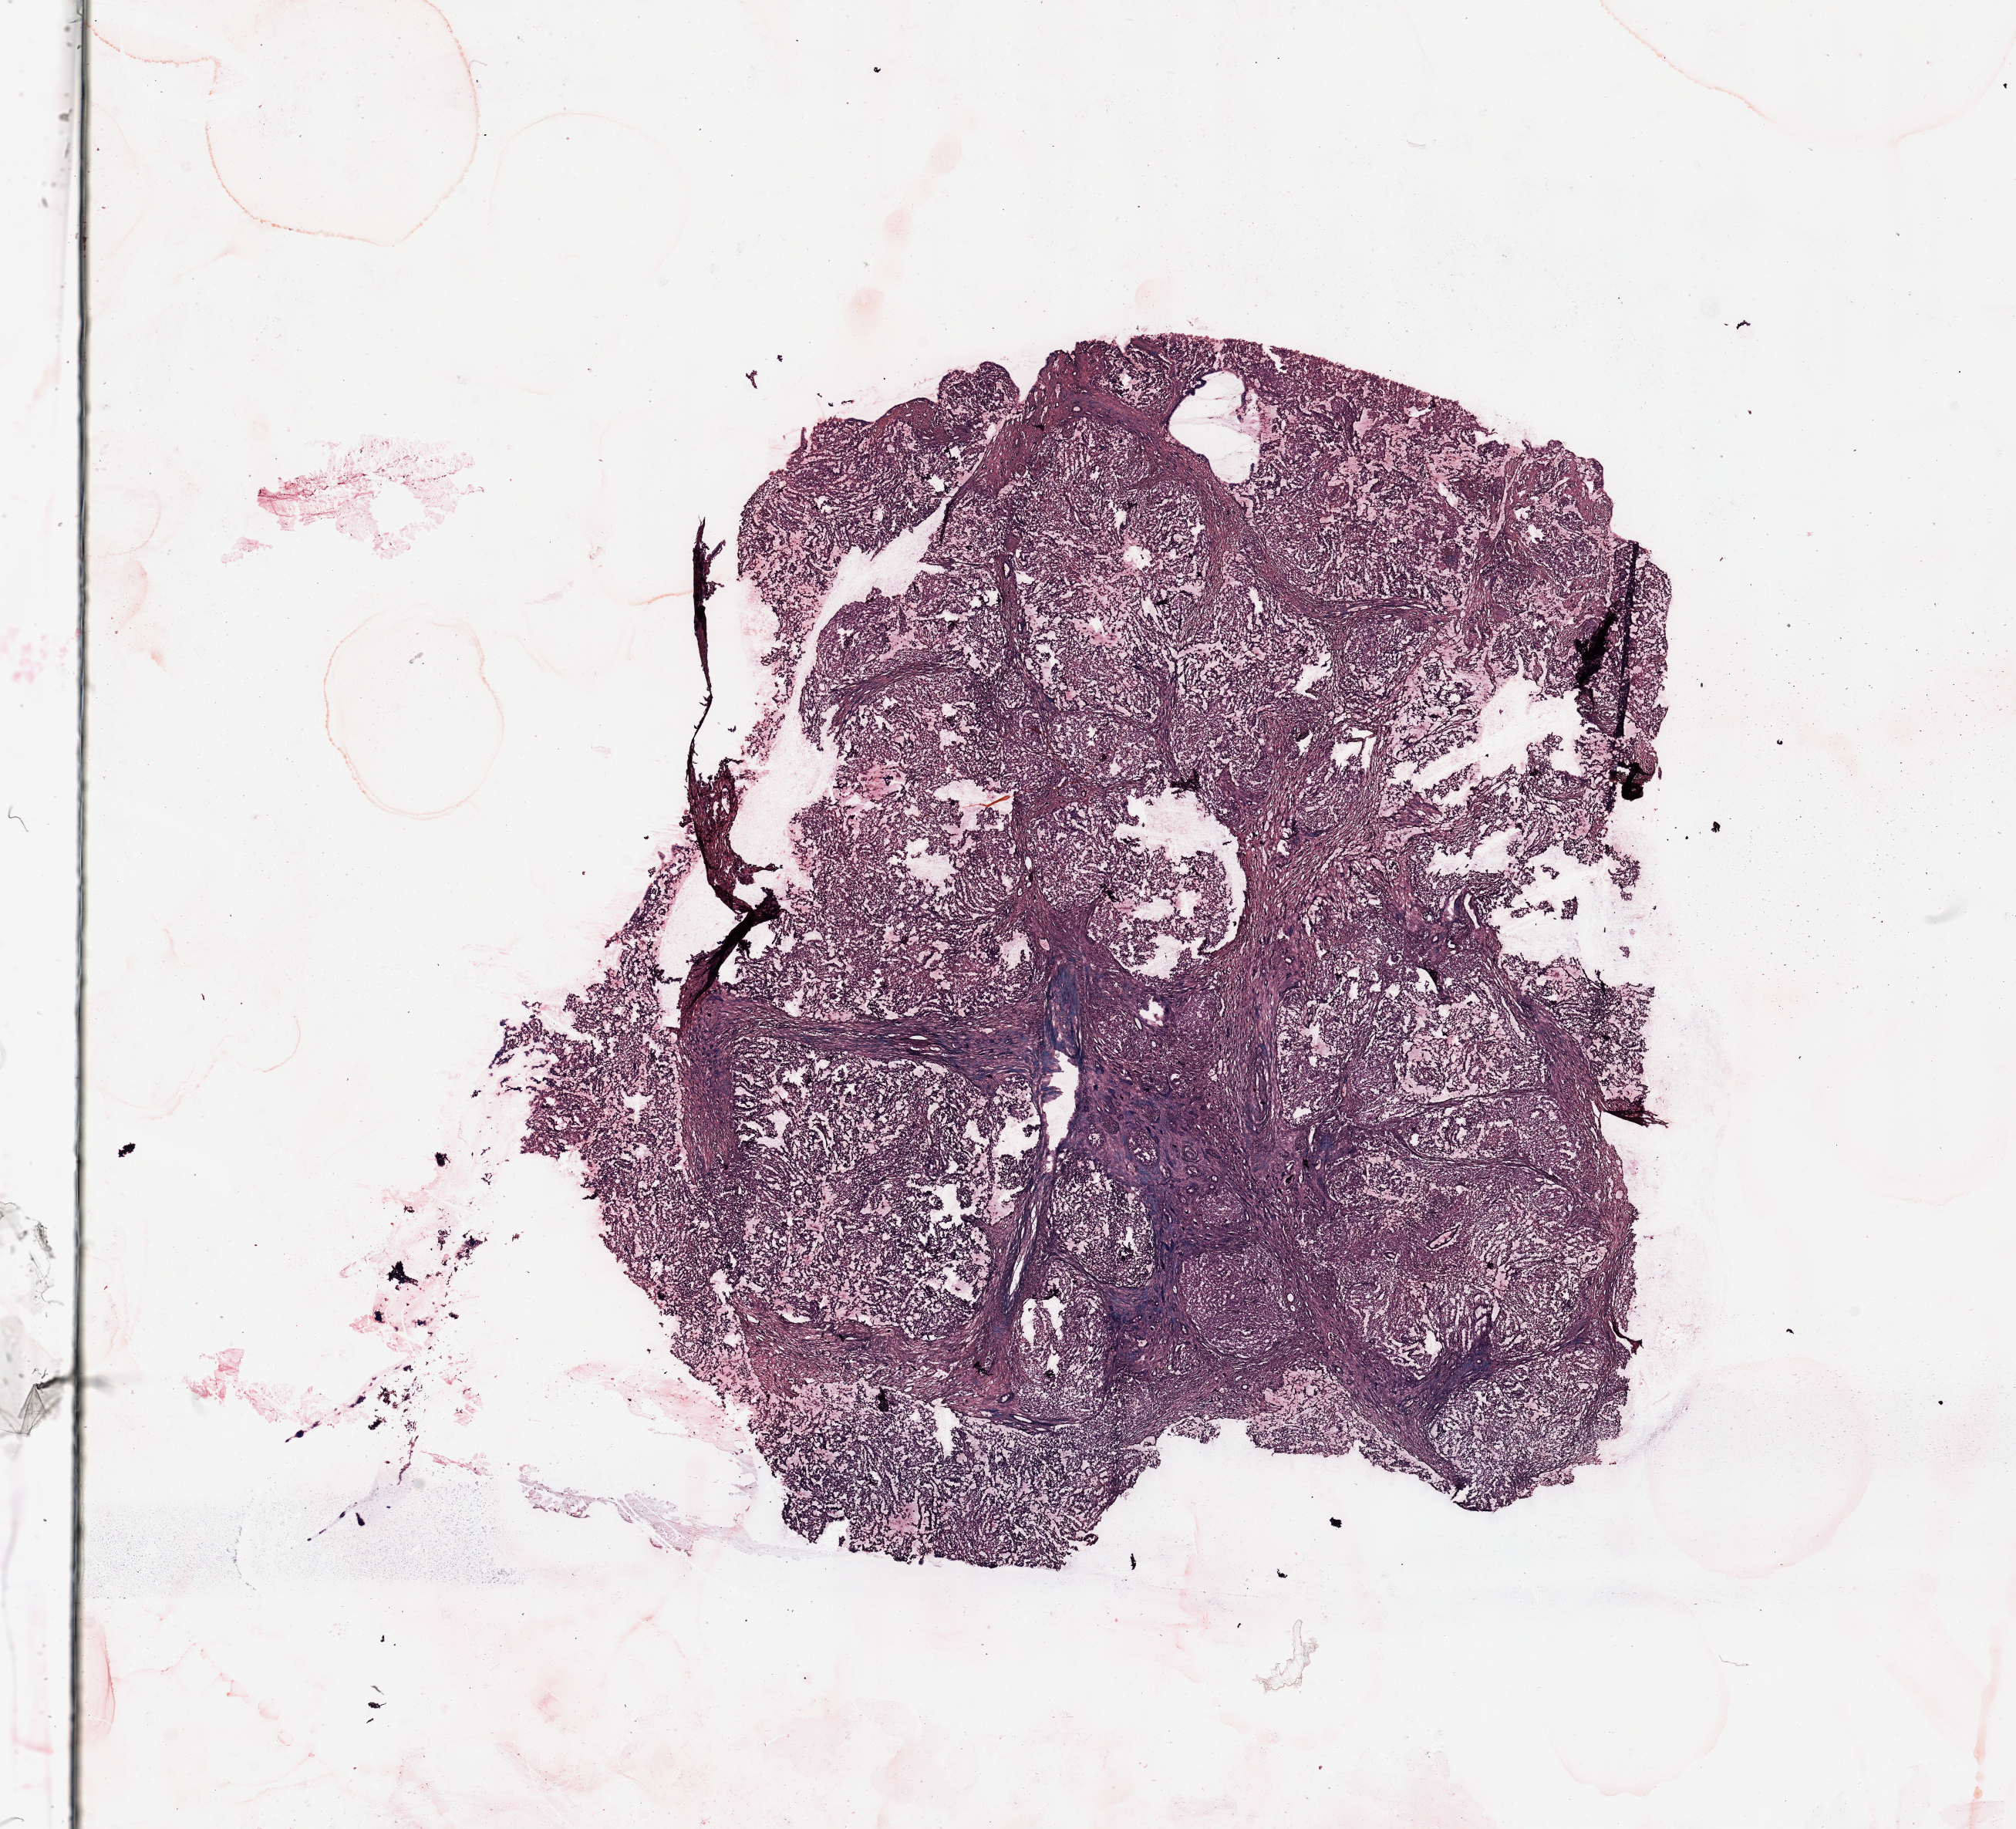
H&E-stained whole-slide image — whole scanned area (about 20.7 x 18.8 mm, acquisition: 20x scan) shown as a low-resolution overview, tumour tissue sample, sampled site: kidney. Male, 72 y/o. Histologic grade: G3 (poorly differentiated). Slide review estimates, as recorded: tumour nuclei 90%, necrosis 5%.
Diagnosis: Renal cell carcinoma, NOS. AJCC pathologic stage: III. Primary tumour site (as recorded): upper pole.